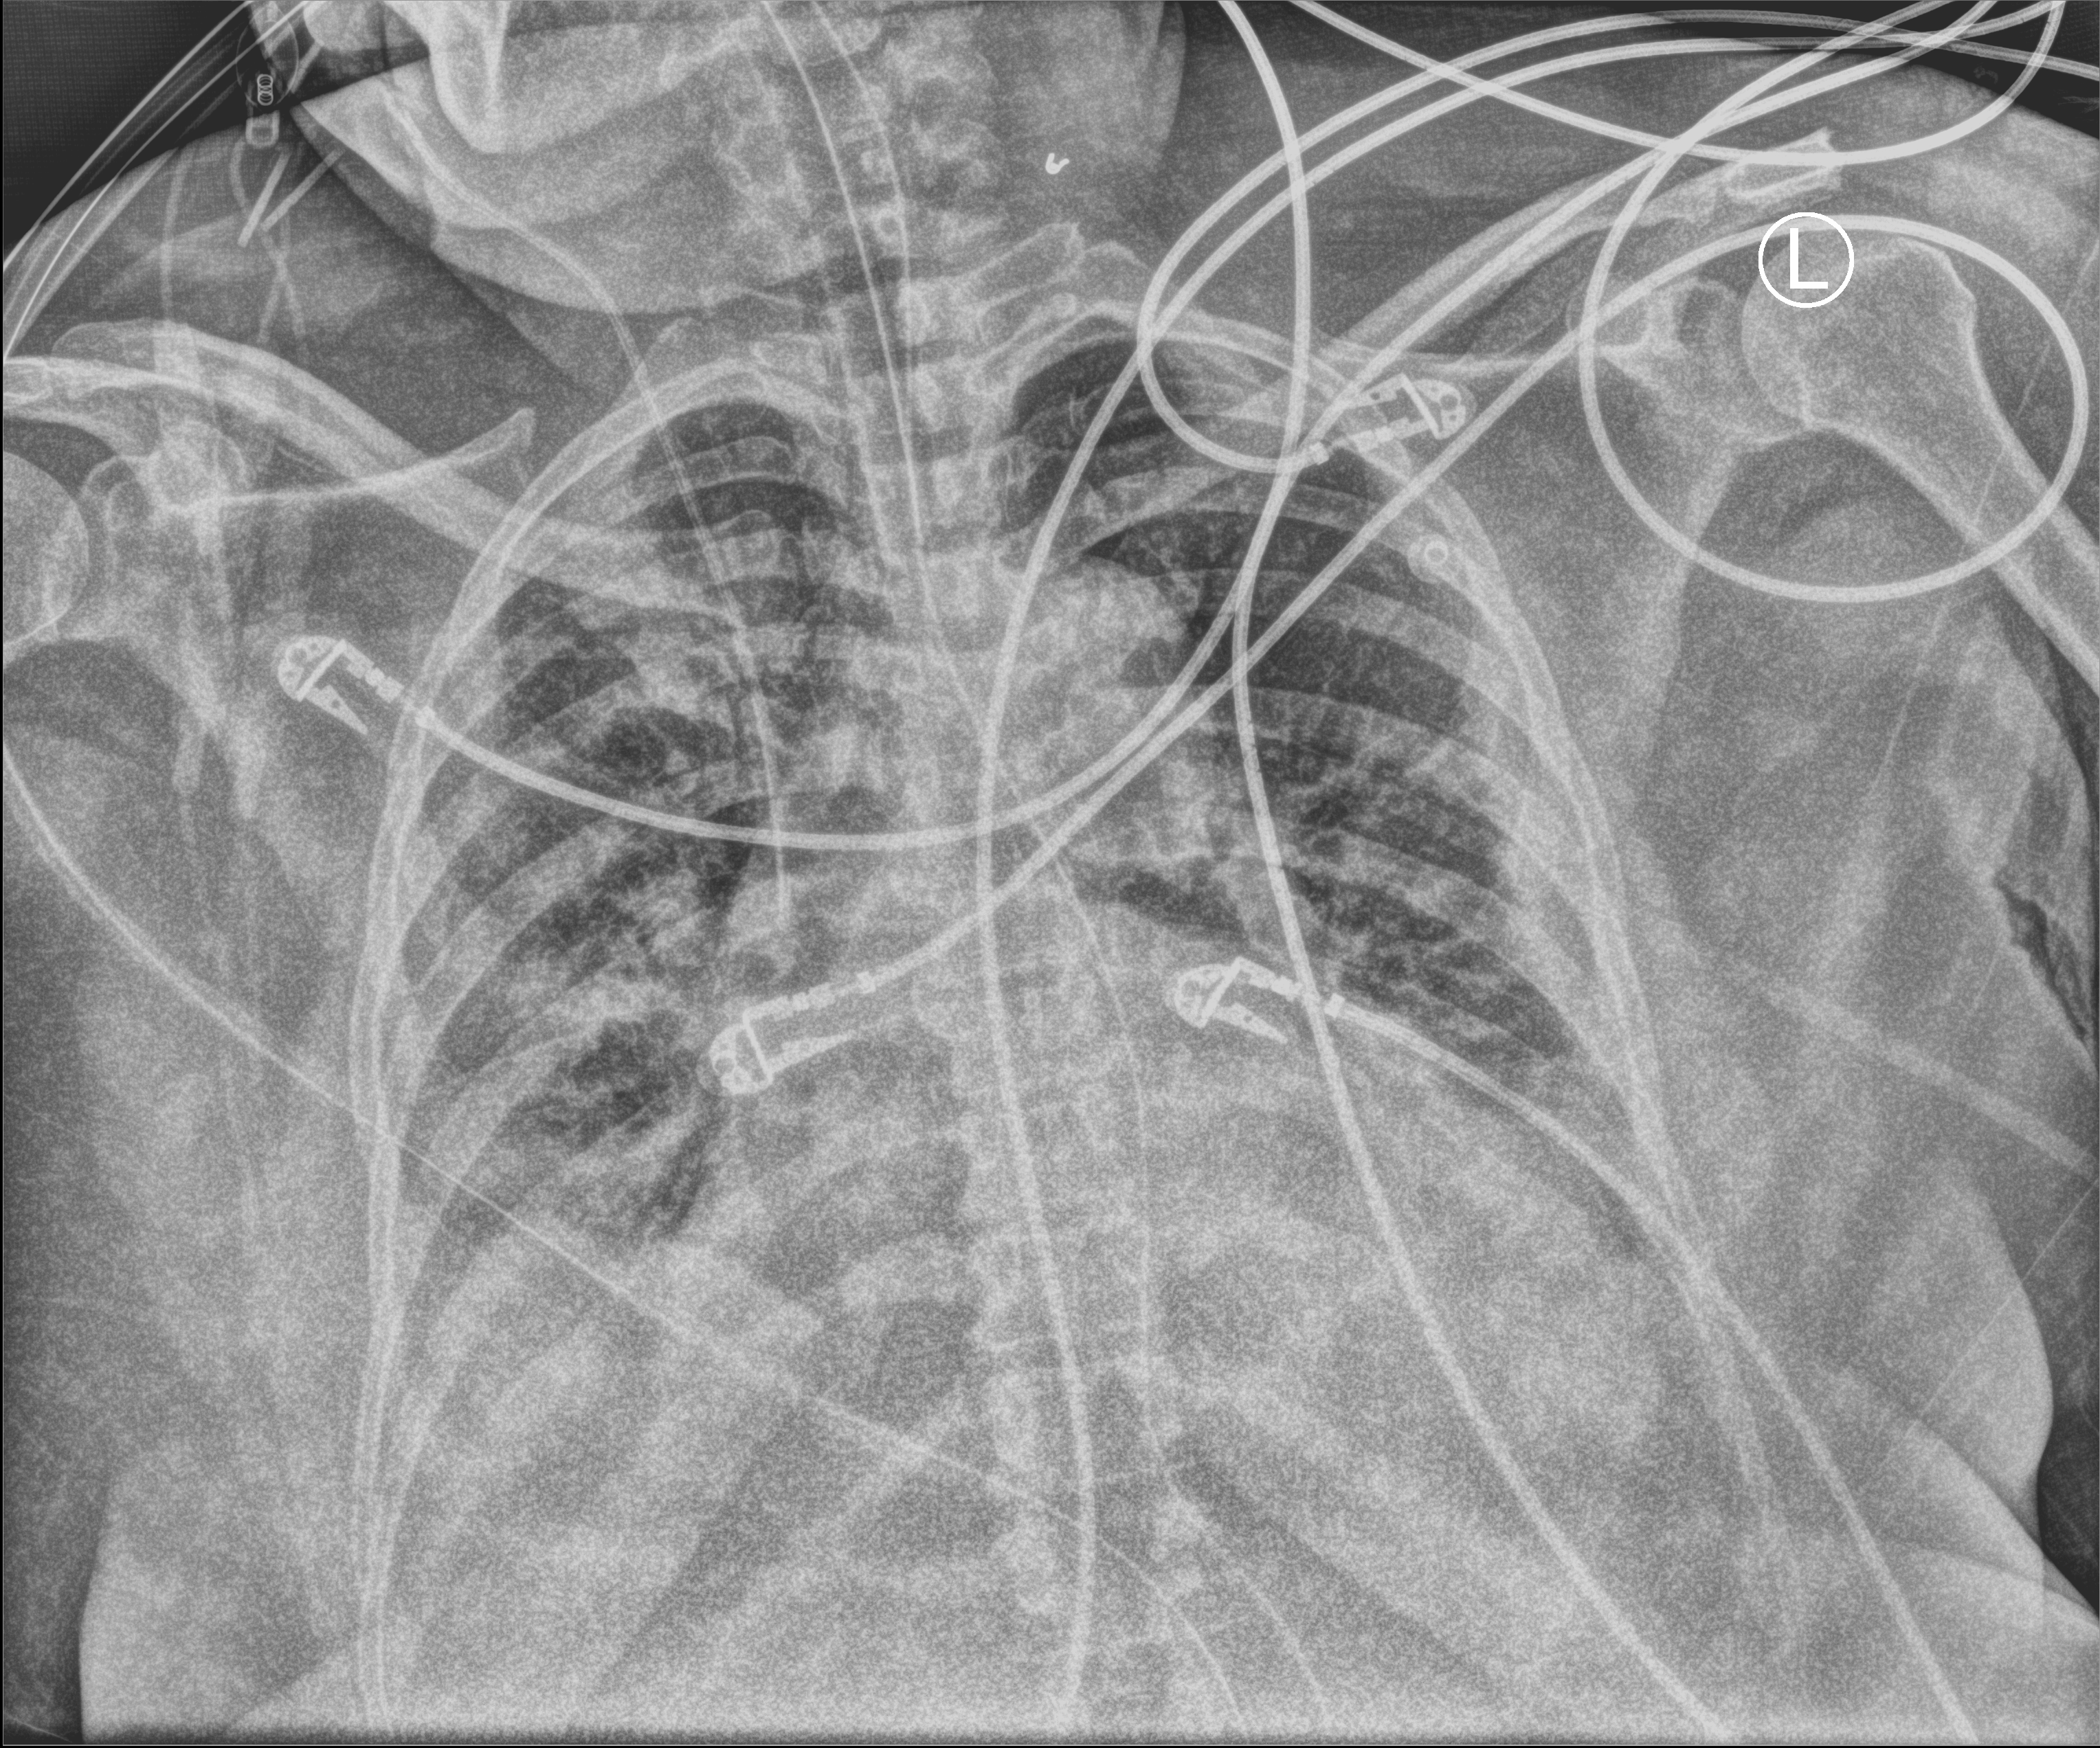
Portable chest radiograph; anteroposterior (AP) projection. Female patient hospitalised with COVID-19, age 60–74 years.
From the hospital-stay record, not from the radiograph (when in the stay this image was taken is not recorded):
- mechanically ventilated during this hospital stay: yes
- diabetes (admission record): yes
- COPD (admission record): no